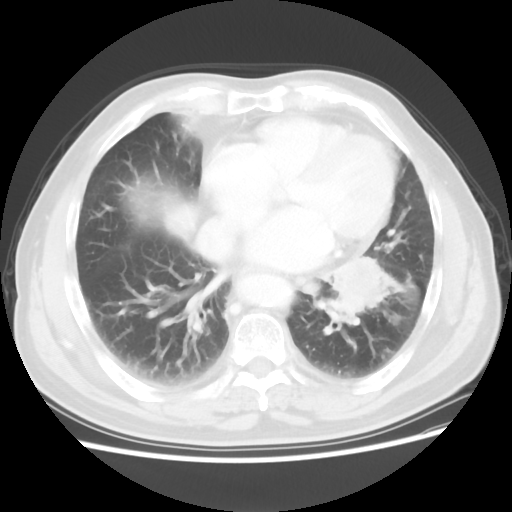
Chest CT, one axial slice; position 24 of 56 along the scan axis; lung window (W 1500 / L -600 HU); 5 mm slice thickness; 512 × 512 image matrix, field of view 360 × 360 mm. Male patient, age 75 years. From the clinical record (not read from this slice): clinical TNM (as recorded): T3 N0 M0.
Outlined on this slice (bounding box drawn by a radiologist):
- lung tumour (recorded histology: squamous cell carcinoma): box from (x=322, y=256) to (x=401, y=326) px